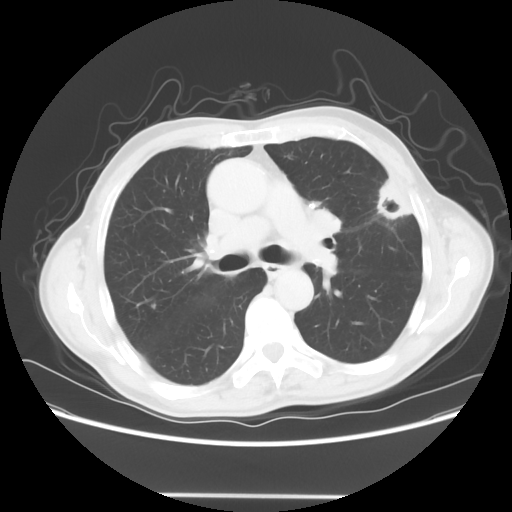
Chest CT, one axial slice. Position 39 of 64 along the scan axis. Reconstruction kernel STANDARD. 120 kVp. Lung window (W 1500 / L -600 HU). 5 mm slice thickness. 512 × 512 image matrix. Male patient, age 71 years. Case-level facts recorded for this patient, not image findings: clinical TNM (as recorded): T1c N0 M0.
Structures marked on this image (rectangle marked by the reading radiologist):
- lung tumour (recorded histology: adenocarcinoma): bounding box <366,171,417,233> (left, top, right, bottom; pixels)